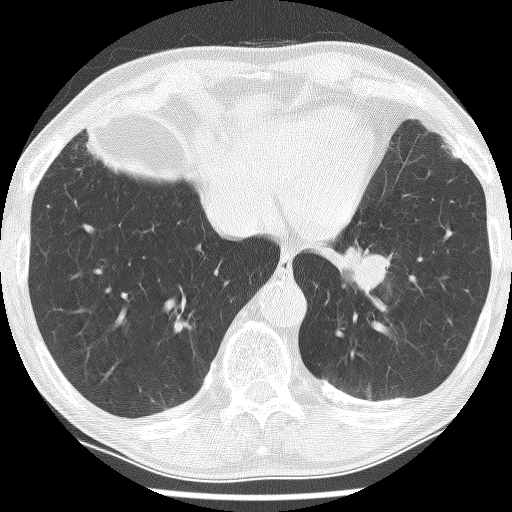
Axial slice from a low-dose chest CT screening exam, baseline annual screen, lung window (W 1500 / L -600 HU), 2.5 mm slice thickness, 120 kVp. Male, age 74 years at enrolment. Current smoker at enrolment.
• Expert-annotated lung lesion, bounding box (x1, y1, x2, y2) in pixels: (313, 217, 414, 309).
• Screening reader's record for this exam (one nodule recorded; not confirmed to be the boxed lesion): non-calcified nodule or mass ≥4 mm, left lower lobe, 30 × 27 mm, spiculated (stellate) margins, soft tissue attenuation.
• Official screen result: positive, change unspecified: nodule(s) >= 4 mm or enlarging nodule(s), mass(es), or other non-specific abnormalities suspicious for lung cancer.
• Participant outcome: lung cancer diagnosed 151 days after this screen — adenocarcinoma, NOS, left lower lobe, stage IIIA (AJCC 6th edition), 49 mm at pathology.